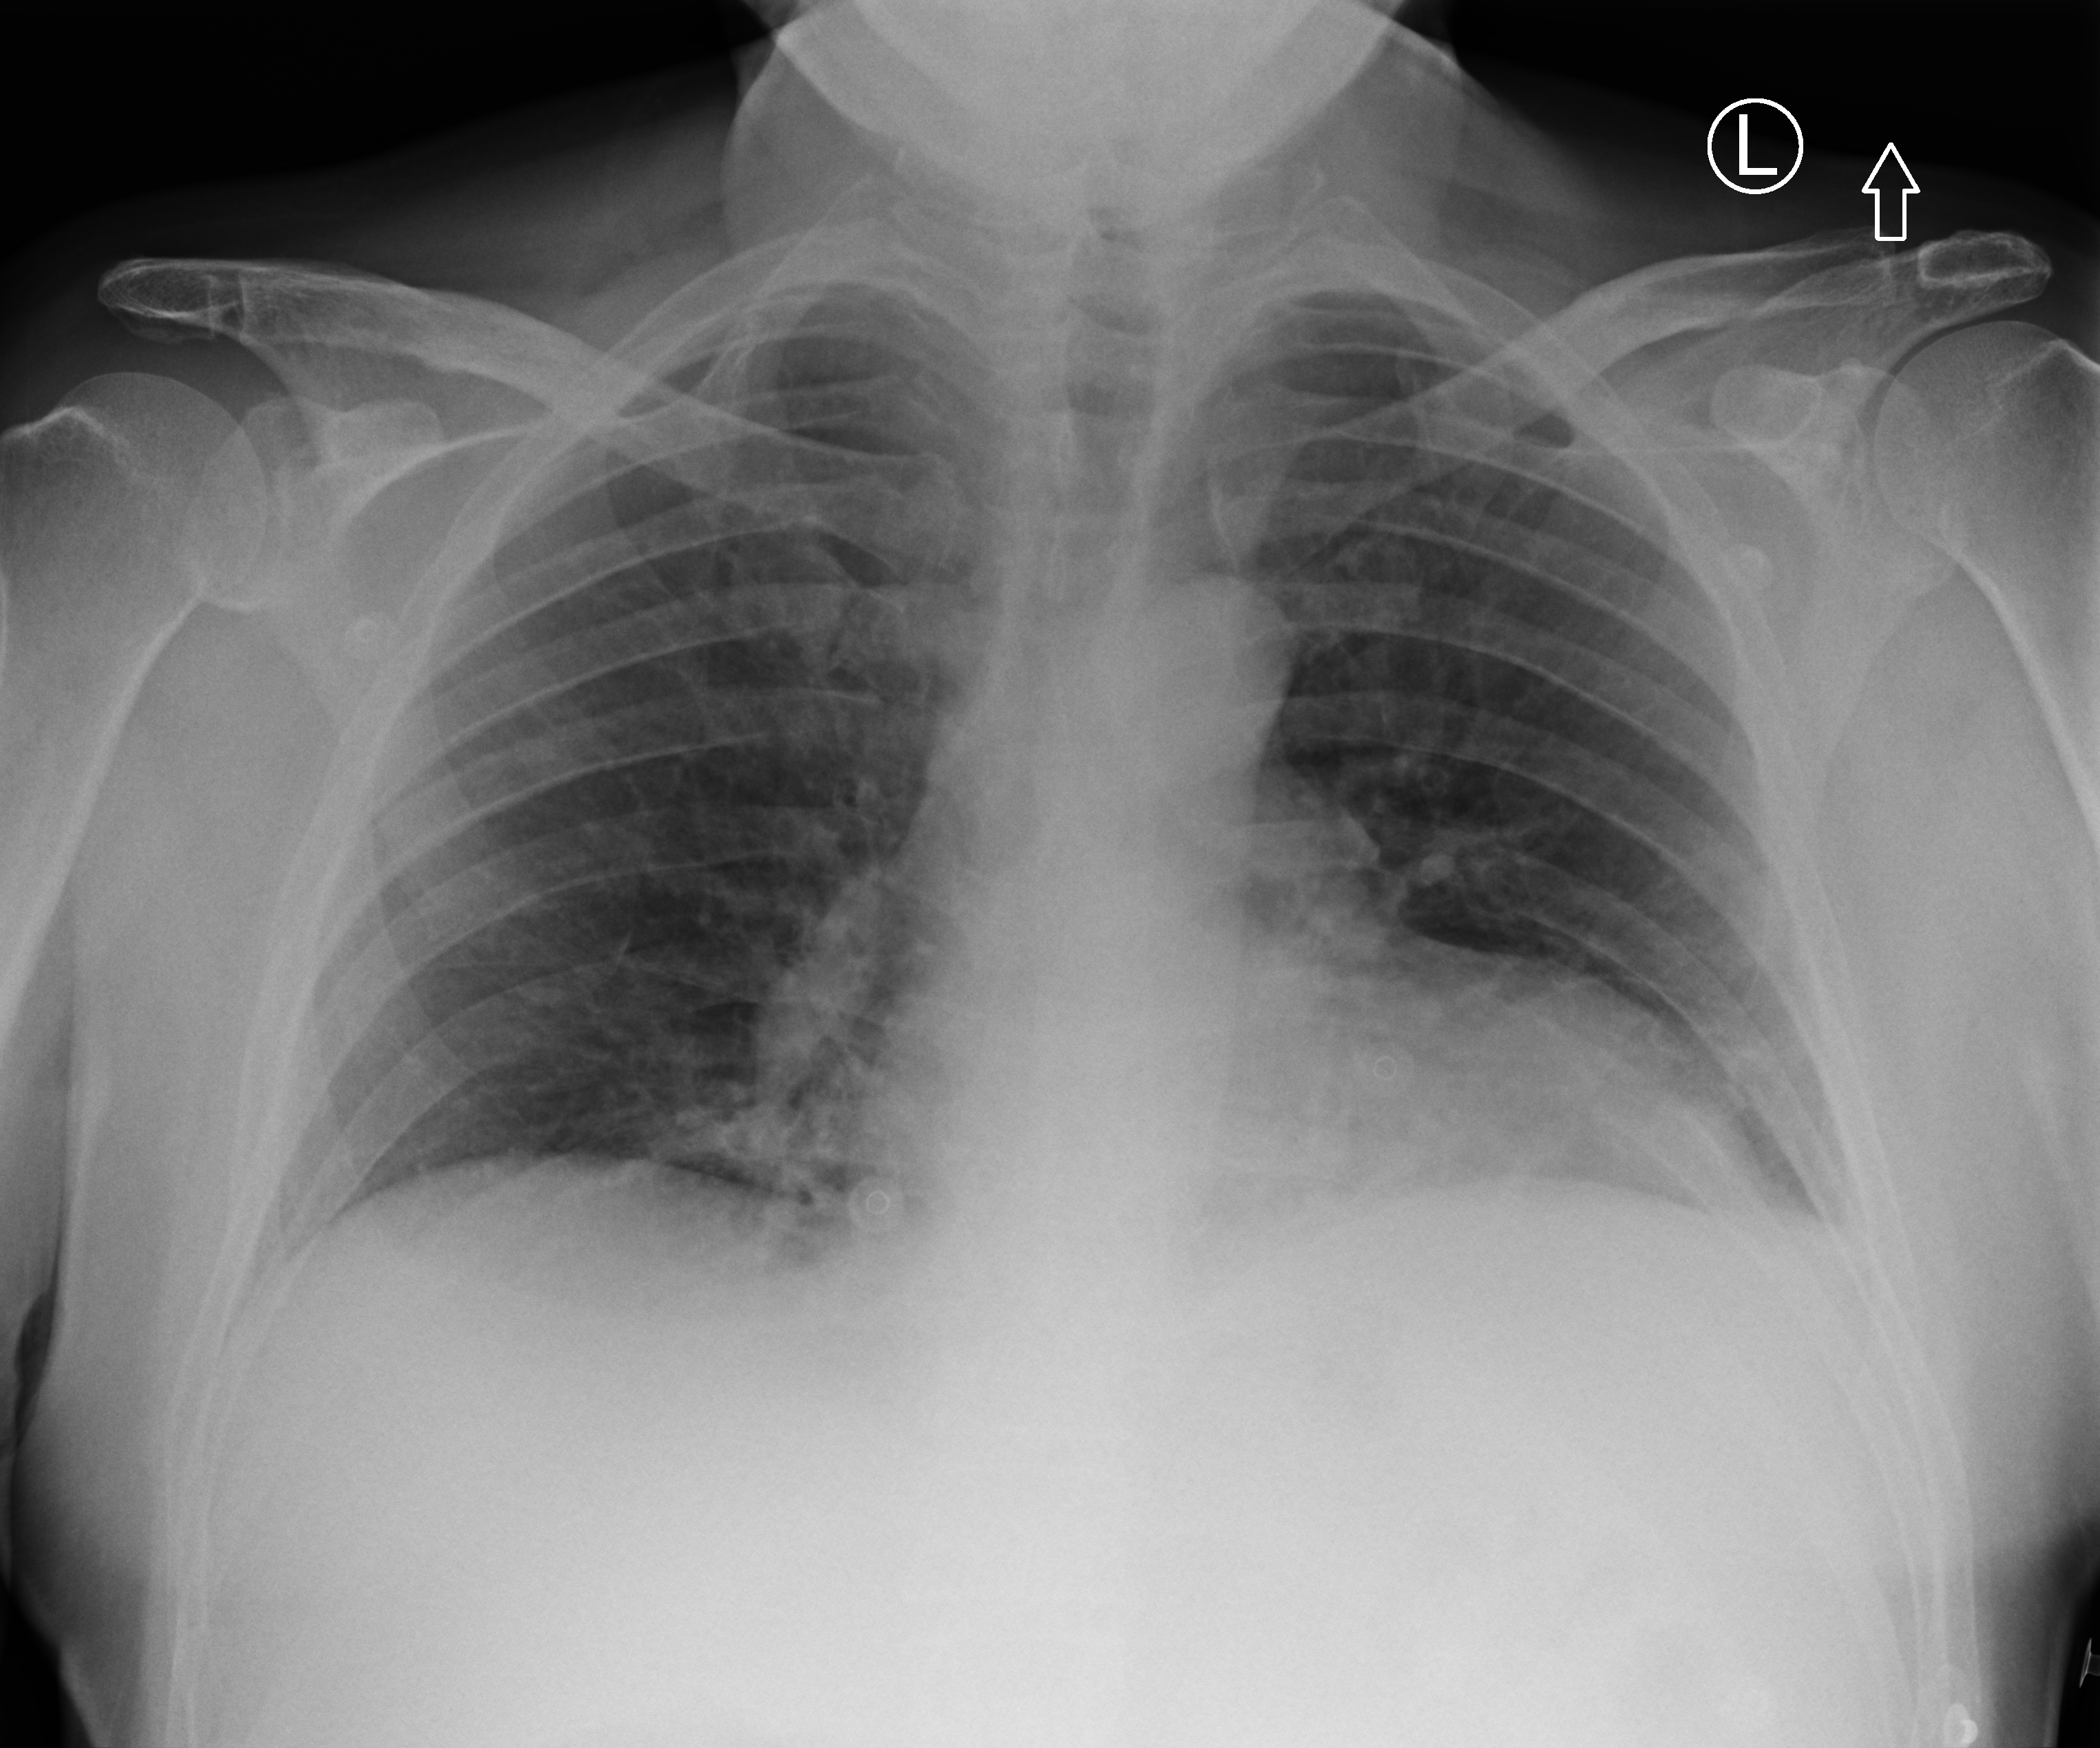
Bedside chest radiograph (computed radiography). Patient hospitalised with COVID-19; male, aged 60–74 years.
From the hospital-stay record, not from the radiograph (when in the stay this image was taken is not recorded): length of hospital stay: 24 days; smoking status (admission record): never; admitted to intensive care during this hospital stay: yes.